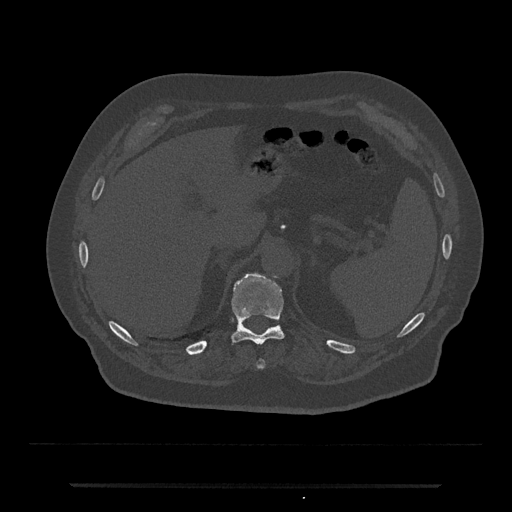
CT including the spine, one axial slice. Slice 650 of 797 in the series (ordered by position). Reconstruction kernel Br40s/3. 120 kVp. Bone window (W 1800 / L 400 HU). 0.5 mm slice thickness. 512 × 512 image matrix, field of view 434 × 434 mm. Male patient, age 80 years. From the clinical record (not read from this slice): primary cancer: prostate.
Outlined on this slice (semi-automatically segmented with operator editing):
- T10 vertebra: bounding box <257,359,265,368> (left, top, right, bottom; pixels)
- T11 vertebra: <231,274,284,345>